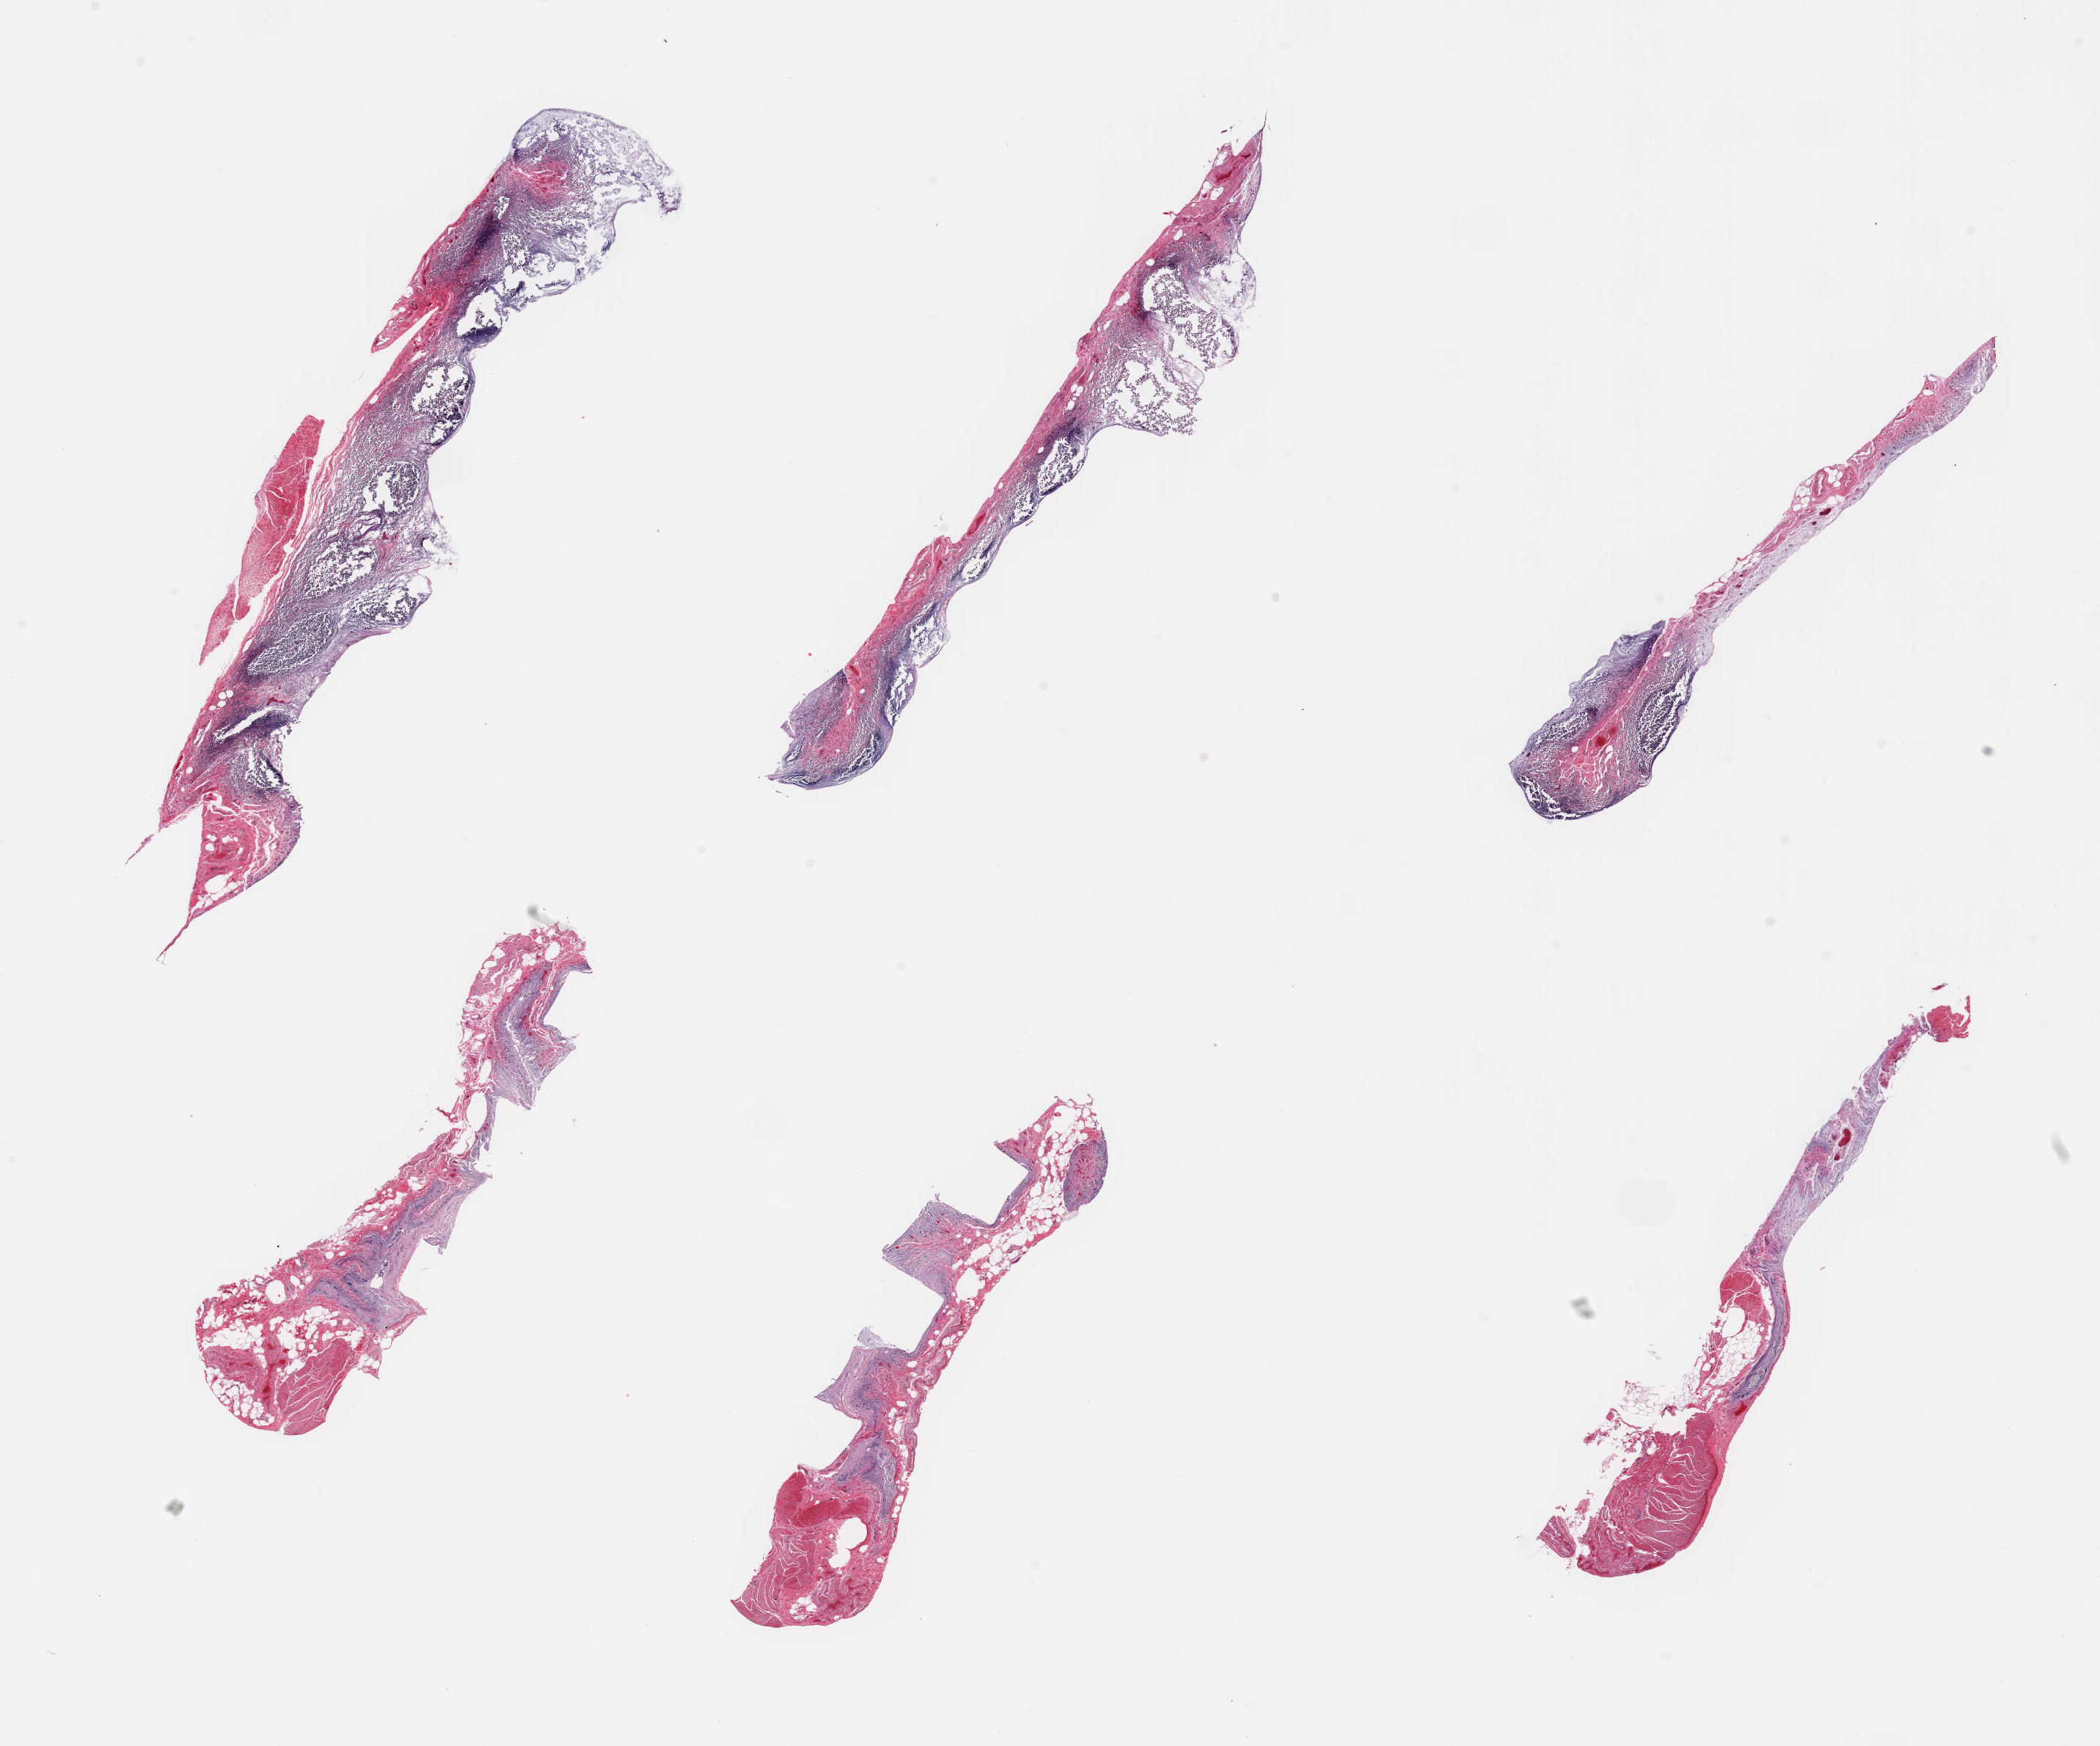
Digitized hematoxylin and eosin (H&E)-stained section, brightfield, whole scanned area (about 22.6 x 18.8 mm, from a 20x scan) shown as a low-resolution overview. PAXgene-fixed paraffin-embedded (PFPE) section. Section of ileum (target tissue). Tissue donor sample. Male donor.
Review note (as recorded): 6 pieces; significant component of targeted lymphoid tissue, but too autolyzed, also includes muscularis (not target).